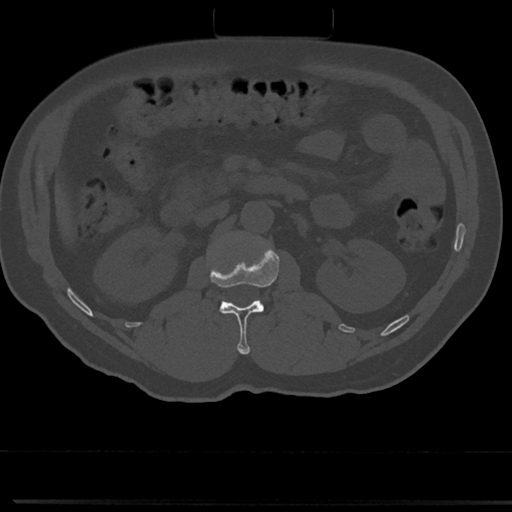
CT including the spine, one axial slice. Position 64 of 817 along the scan axis. Reconstruction kernel Br40s/3. 120 kVp. Bone window (W 1800 / L 400 HU). 512 × 512 image matrix. Patient: male, 61 years. Case-level facts recorded for this patient, not image findings: primary cancer: prostate.
Structures marked on this image (semi-automatically segmented with operator editing):
- L1 vertebra: bounding box (x1, y1, x2, y2) in pixels: (208, 240, 279, 354)